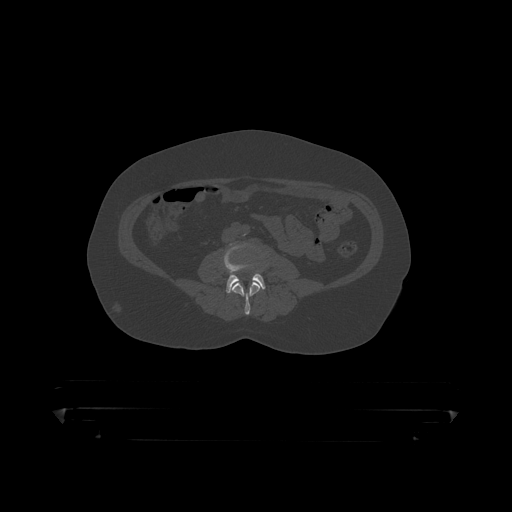
CT including the spine, one axial slice; slice 77 of 390 in the series (ordered by position); reconstruction kernel STANDARD; 120 kVp; bone window (W 1800 / L 400 HU); 512 × 512 image matrix, field of view 650 × 650 mm. Patient: male, 60 years. Case-level facts recorded for this patient, not image findings: primary cancer: prostate.
Outlined on this slice (semi-automatically segmented with operator editing):
- L3 vertebra: box from (x=230, y=264) to (x=266, y=316) px
- L4 vertebra: (x=225, y=256)–(x=265, y=293)